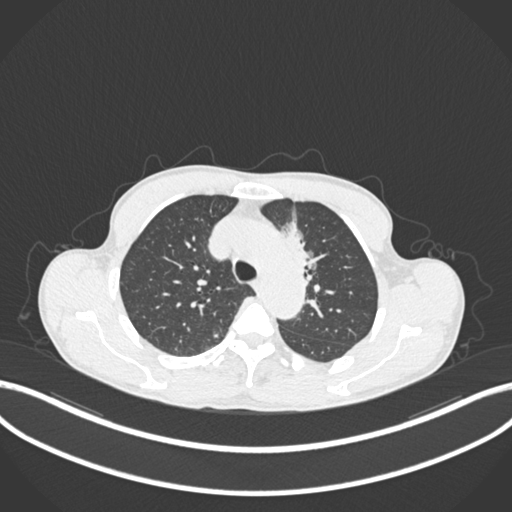
Chest CT, one axial slice; position 149 of 211 along the scan axis; reconstruction kernel B30f; 120 kVp; lung window (W 1500 / L -600 HU); 1 mm slice thickness; 512 × 512 image matrix. Male patient, age 58 years. From the clinical record (not read from this slice): clinical TNM (as recorded): T1c N1 M0.
Structures marked on this image (bounding box drawn by a radiologist):
- lung tumour (recorded histology: adenocarcinoma): bounding box (x1, y1, x2, y2) in pixels: (281, 213, 322, 280)